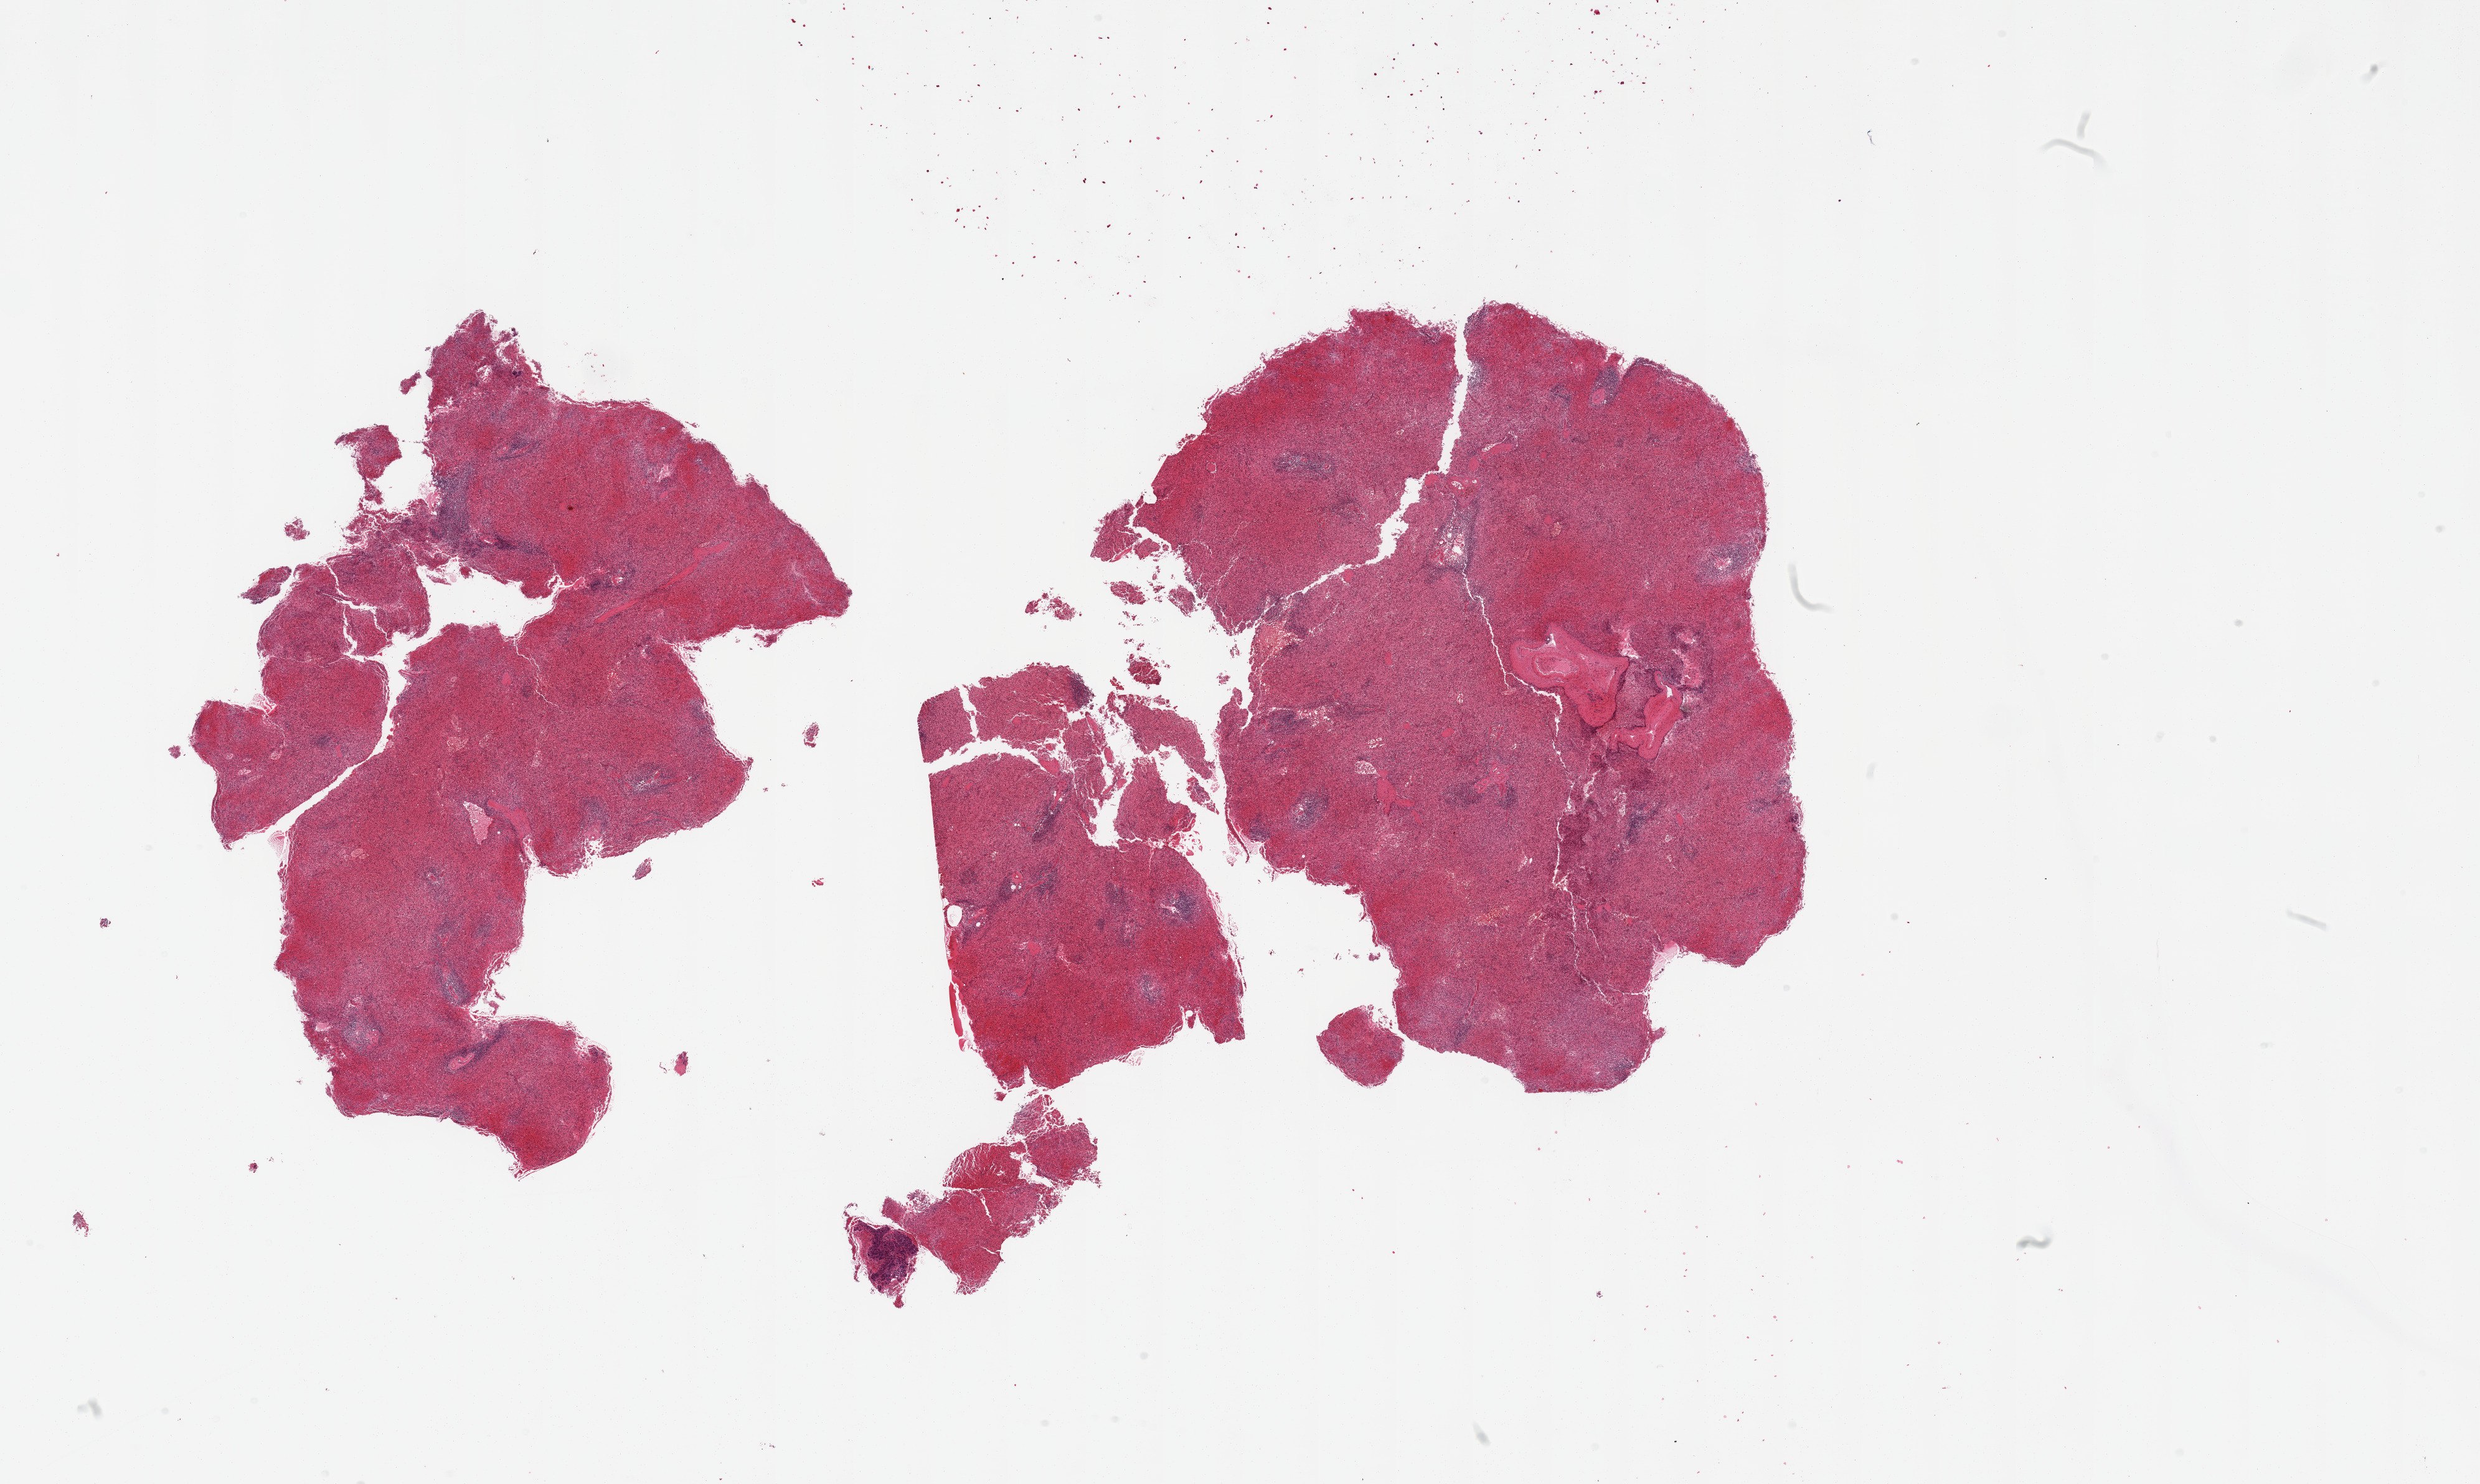
Digitized haematoxylin and eosin-stained section, brightfield — low-resolution overview of the scanned area, about 31.5 x 18.9 mm. PAXgene-fixed paraffin-embedded (PFPE) section. Target tissue: spleen. Tissue donor sample. Donor sex: male.
Reviewer comment on this tissue sample: 2 fragmented pieces; congestion; 1 mm floater of pancreatic tissue; sparse lymphoid tissue.